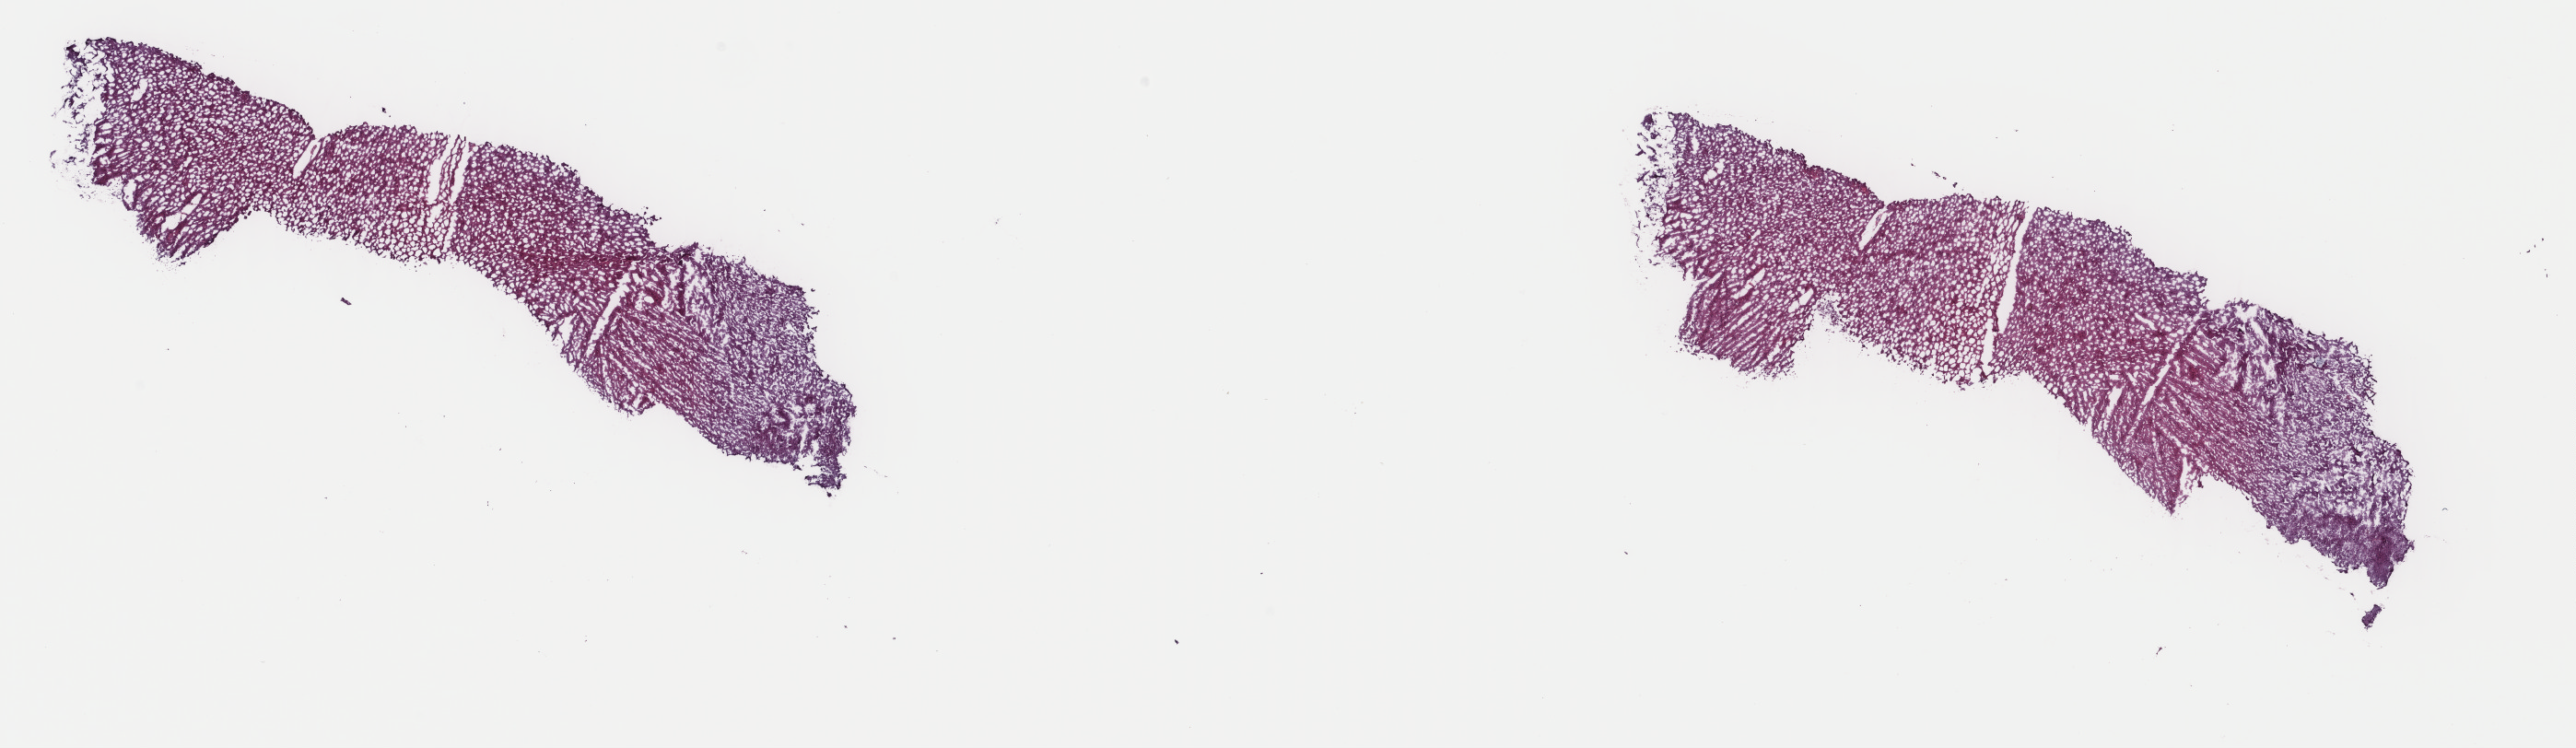
H&E whole-slide image, low-resolution overview of the scanned area, about 22.2 x 6.4 mm (from a 40x scan). Frozen section from the top of the tissue portion. Brain, primary tumour sample. Male patient; age at initial diagnosis 51 years. Slide review estimates, as recorded: tumour cells 40%, tumour nuclei 70%, normal cells 10%, stromal cells 50%, necrosis 0%. Inflammatory infiltration, as recorded: lymphocyte infiltration 0%, monocyte infiltration 0%, neutrophil infiltration 0%.
- pathologic diagnosis: Glioblastoma (frontal lobe)